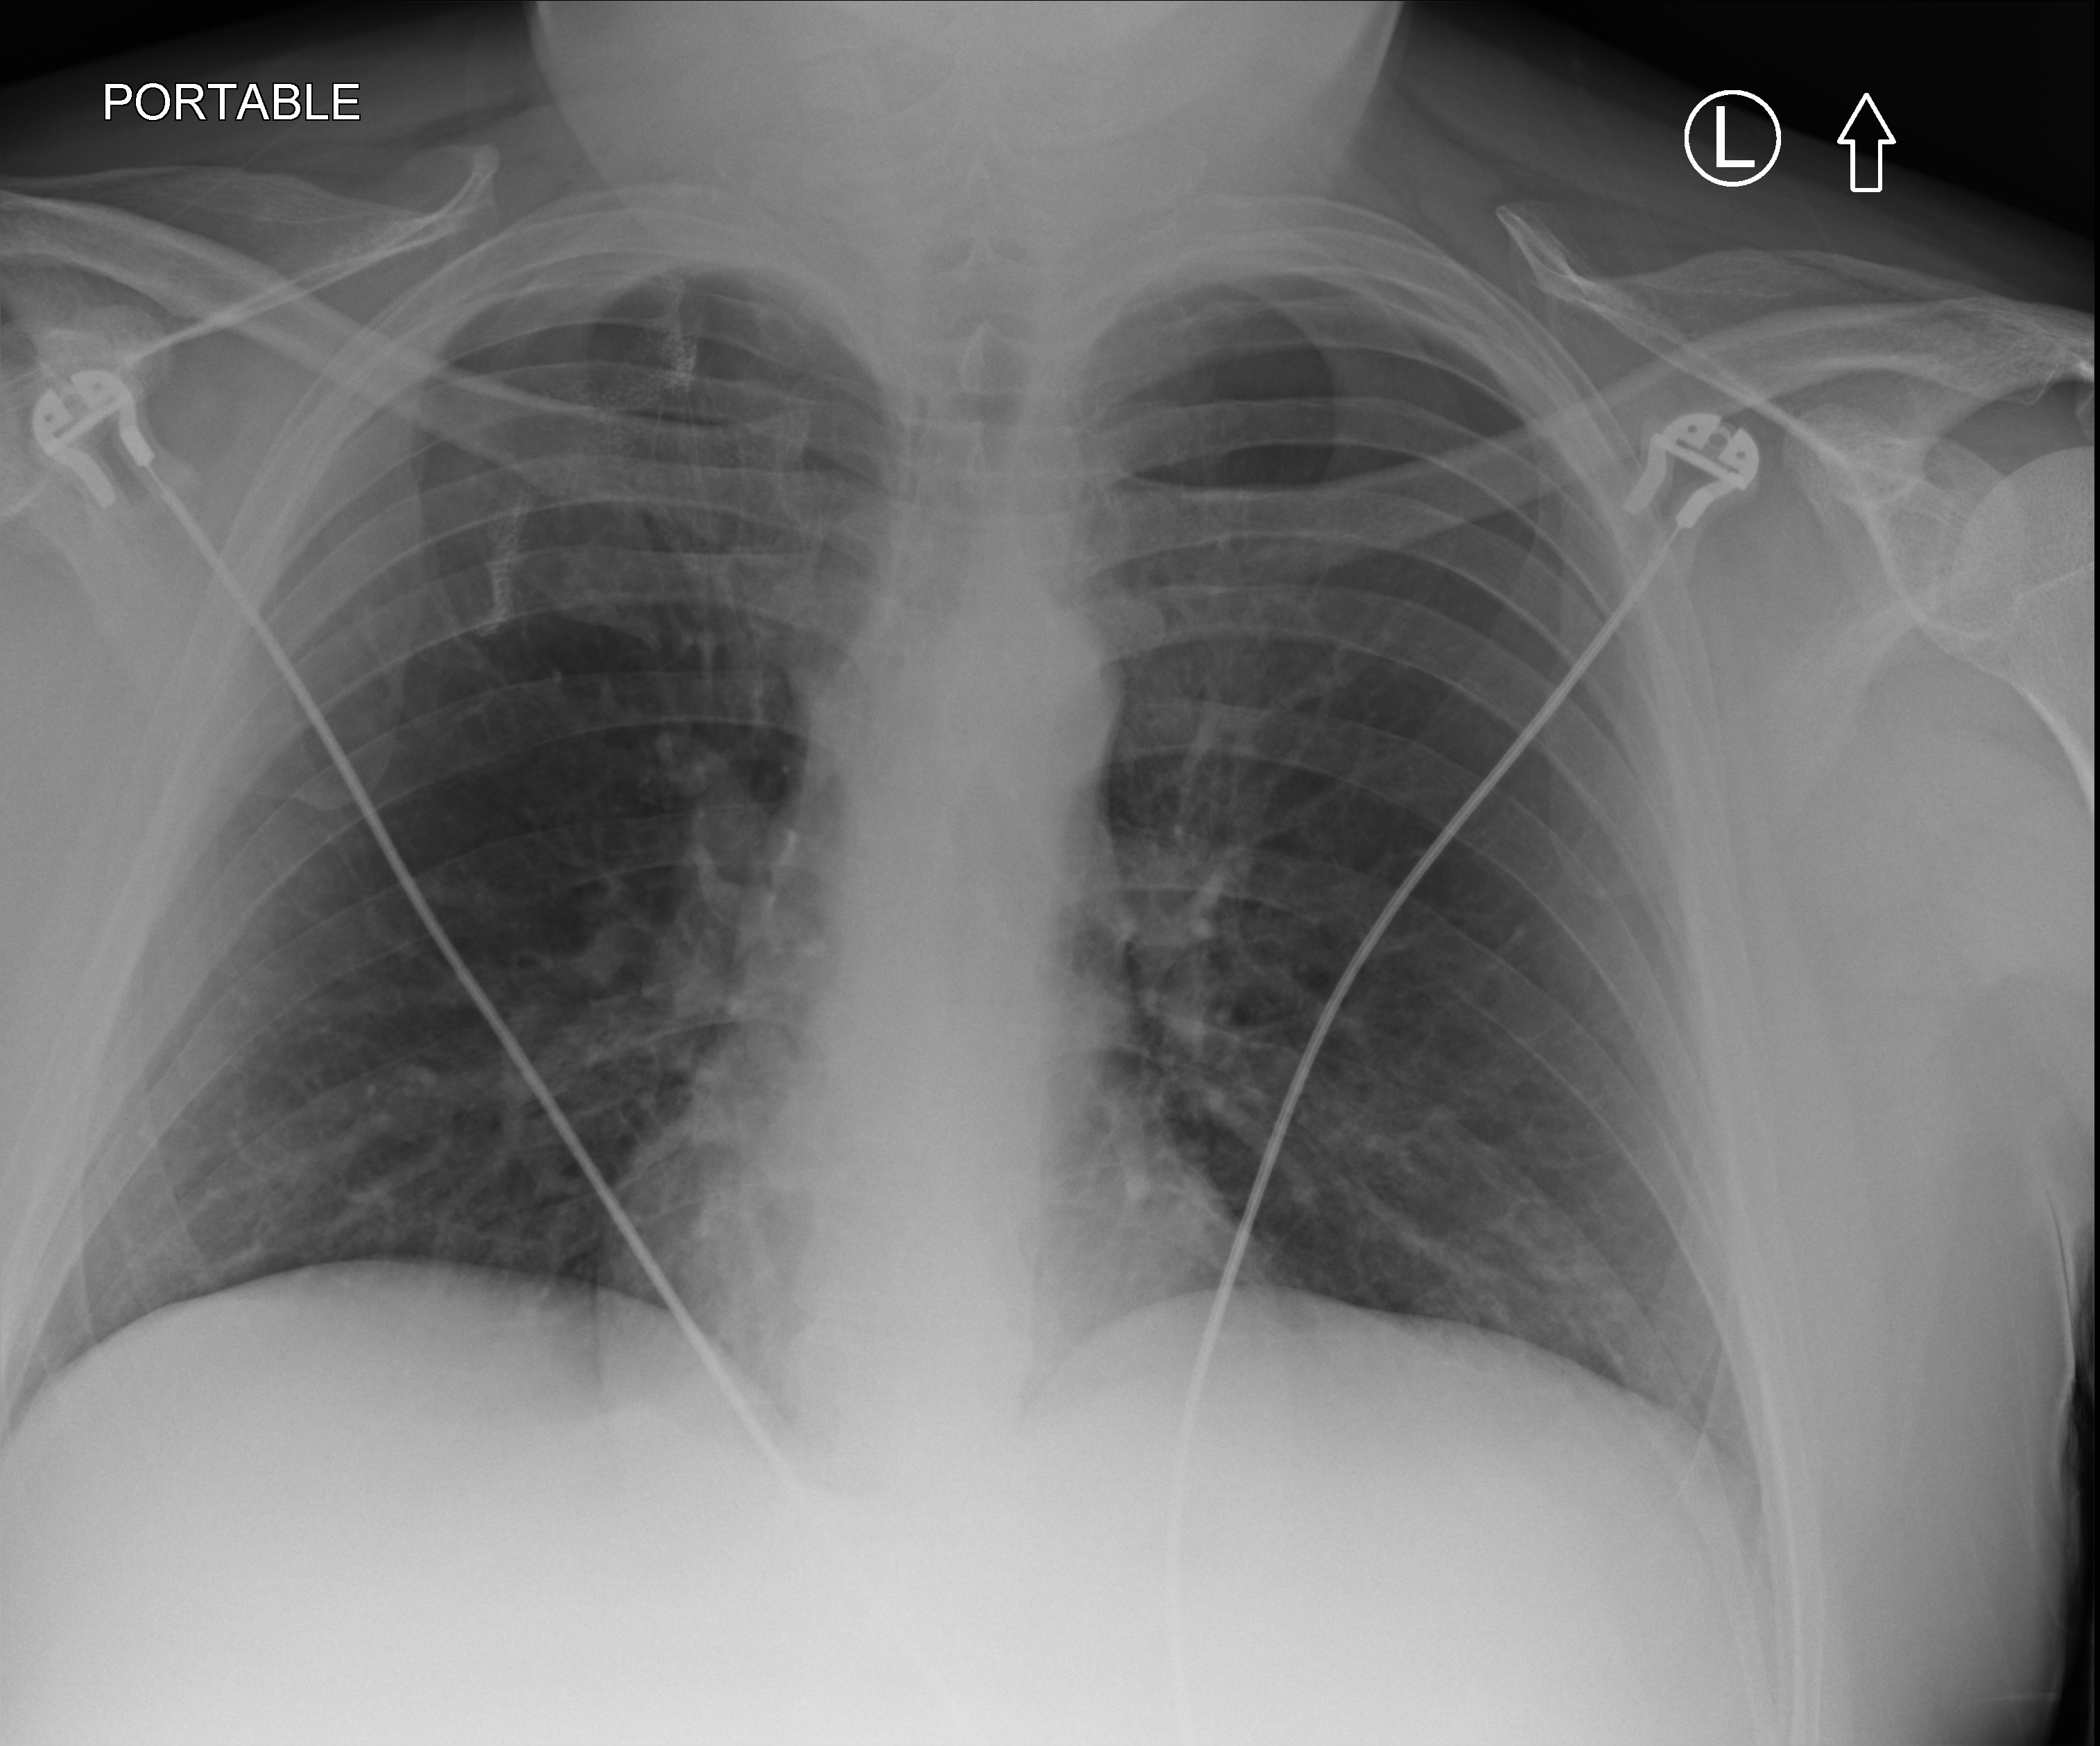
Portable chest radiograph, anteroposterior (AP) projection. Patient hospitalised with COVID-19; male, aged 18–59 years.
Hospital-stay facts (about this admission, not read from this image; timing relative to this image not recorded):
- admitted to intensive care during this hospital stay: no